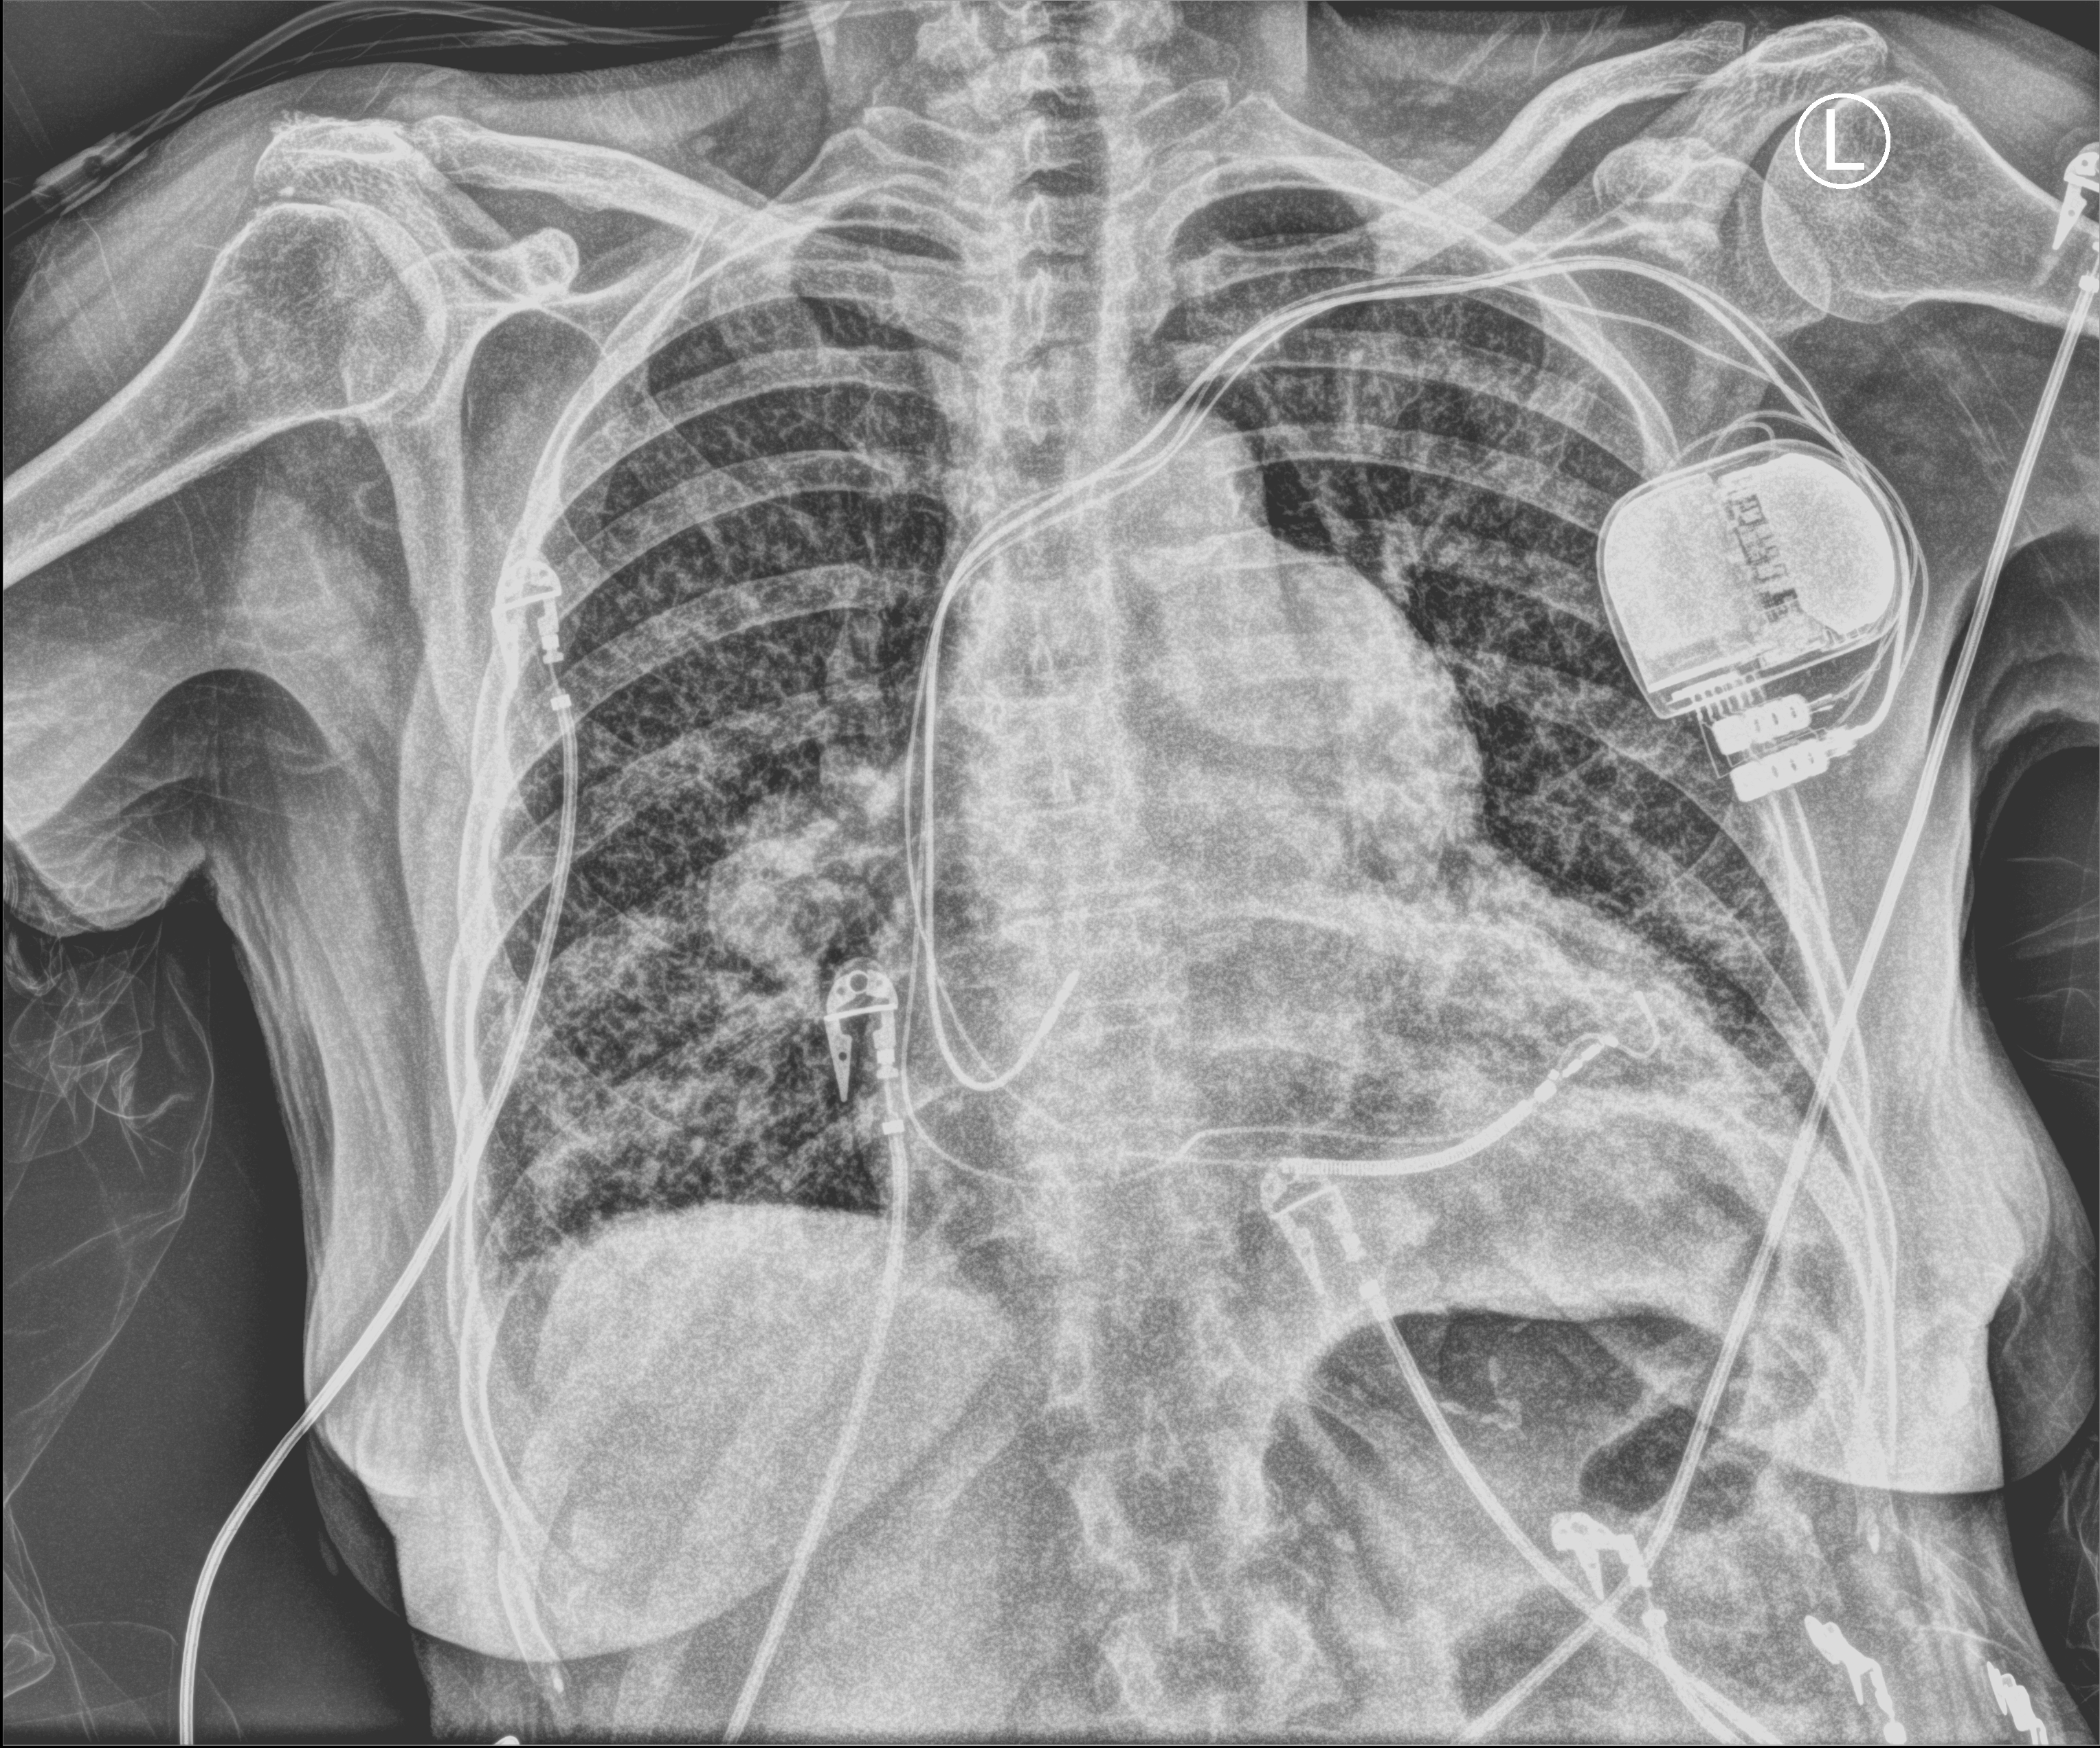
Bedside chest radiograph (computed radiography); anteroposterior (AP) projection. Female patient hospitalised with COVID-19, age 60–74 years.
From the hospital-stay record, not from the radiograph (when in the stay this image was taken is not recorded):
- admitted to intensive care during this hospital stay: yes
- length of hospital stay: 6 days
- mechanically ventilated during this hospital stay: no